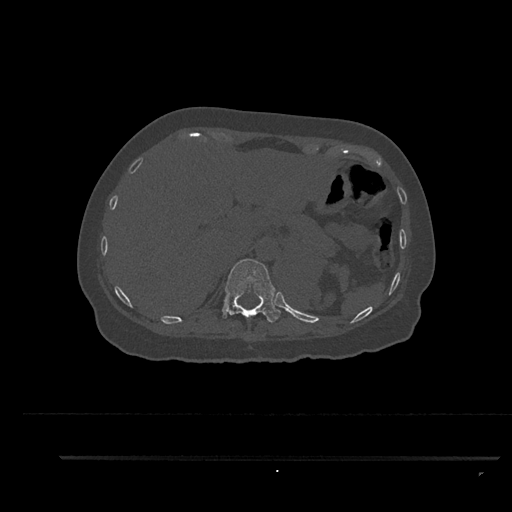
CT including the spine, one axial slice; position 319 of 797 along the scan axis; 120 kVp; bone window (W 1800 / L 400 HU); 512 × 512 image matrix. Patient: female, 44 years. From the clinical record (not read from this slice): primary cancer: renal.
Structures marked on this image (semi-automatic segmentation, software-assisted and operator-edited):
- T11 vertebra: box from (x=222, y=259) to (x=281, y=323) px